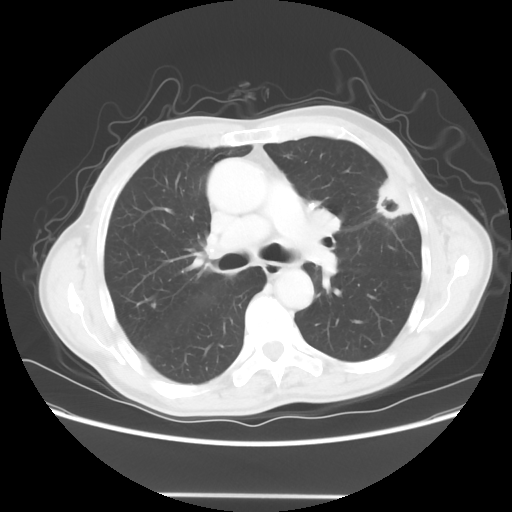
Chest CT, one axial slice; position 39 of 64 along the scan axis; reconstruction kernel STANDARD; lung window (W 1500 / L -600 HU); 5 mm slice thickness; 512 × 512 image matrix. Male patient, age 71 years. Case-level facts recorded for this patient, not image findings: clinical TNM (as recorded): T1c N0 M0; histopathological grade: G2-3.
Structures marked on this image (rectangle marked by the reading radiologist):
- lung tumour (recorded histology: adenocarcinoma): bounding box (x1, y1, x2, y2) in pixels: (367, 172, 422, 221)